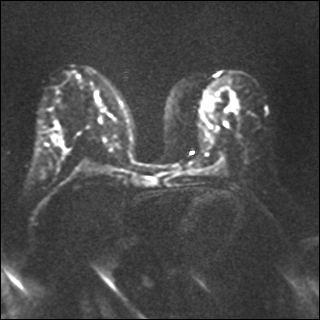
Breast MRI, one axial slice; slice 17 of 35 in the series (ordered by position); diffusion-weighted series; image 2 of 4 stored at this slice position (different b-values; order by instance number); 1.5 T; 4 mm slice thickness; 320 × 320 image matrix. Female patient.
Outlined on this slice (expert manual segmentation):
- tumour on diffusion-weighted imaging: bounding box <225,122,227,126> (left, top, right, bottom; pixels)